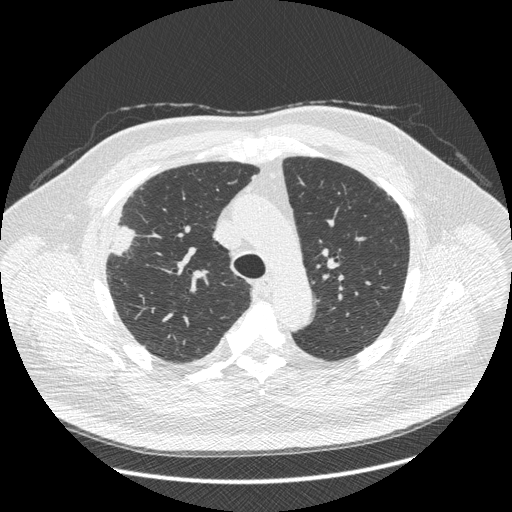
Axial slice from a low-dose chest CT screening exam, third annual screen, lung window (W 1500 / L -600 HU), slice 120 of 426 in the series. Male participant, aged 66 years at enrolment.
• Expert-annotated lung lesion, bounding box <87,205,147,270> (left, top, right, bottom; pixels).
• Reader record for this screening exam (exam-level; its link to the box is not recorded): non-calcified nodule or mass ≥4 mm, right upper lobe, 48 × 25 mm, spiculated (stellate) margins, soft tissue attenuation, pre-existing on the prior screen: no.
• Lung cancer was diagnosed 35 days after this screen: non-small cell carcinoma, right upper lobe, stage IV (AJCC 6th edition), 50 mm at pathology.